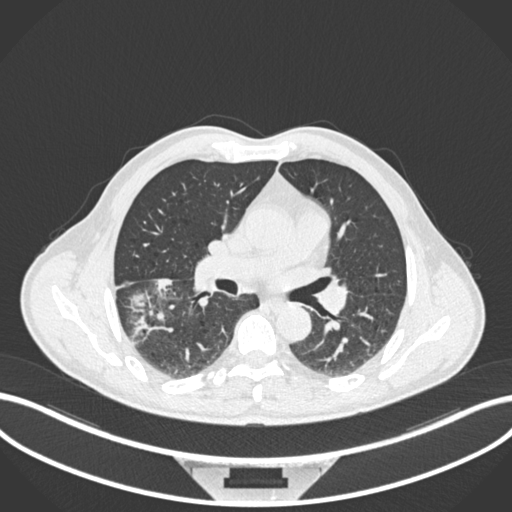
Chest CT, one axial slice; slice 109 of 208 in the series (ordered by position); reconstruction kernel B30f; 120 kVp; lung window (W 1500 / L -600 HU); 1 mm slice thickness; 512 × 512 image matrix. Patient: male, 58 years. Case-level facts recorded for this patient, not image findings: clinical TNM (as recorded): T3 N0 M0; histopathological grade: G2.
Structures marked on this image (bounding box drawn by a radiologist):
- lung tumour (recorded histology: squamous cell carcinoma): bounding box <127,278,173,336> (left, top, right, bottom; pixels)